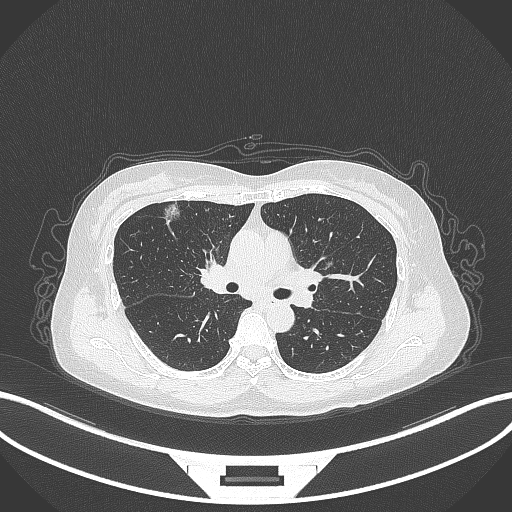
Chest CT, one axial slice. Slice 198 of 315 in the series (ordered by position). Reconstruction kernel B70f. Lung window (W 1500 / L -600 HU). 1 mm slice thickness. 512 × 512 image matrix. Patient: female, 61 years. Case-level facts recorded for this patient, not image findings: clinical TNM (as recorded): T1b N0 M0.
Outlined on this slice (rectangle marked by the reading radiologist):
- lung tumour (recorded histology: adenocarcinoma): bounding box (x1, y1, x2, y2) in pixels: (158, 200, 182, 226)